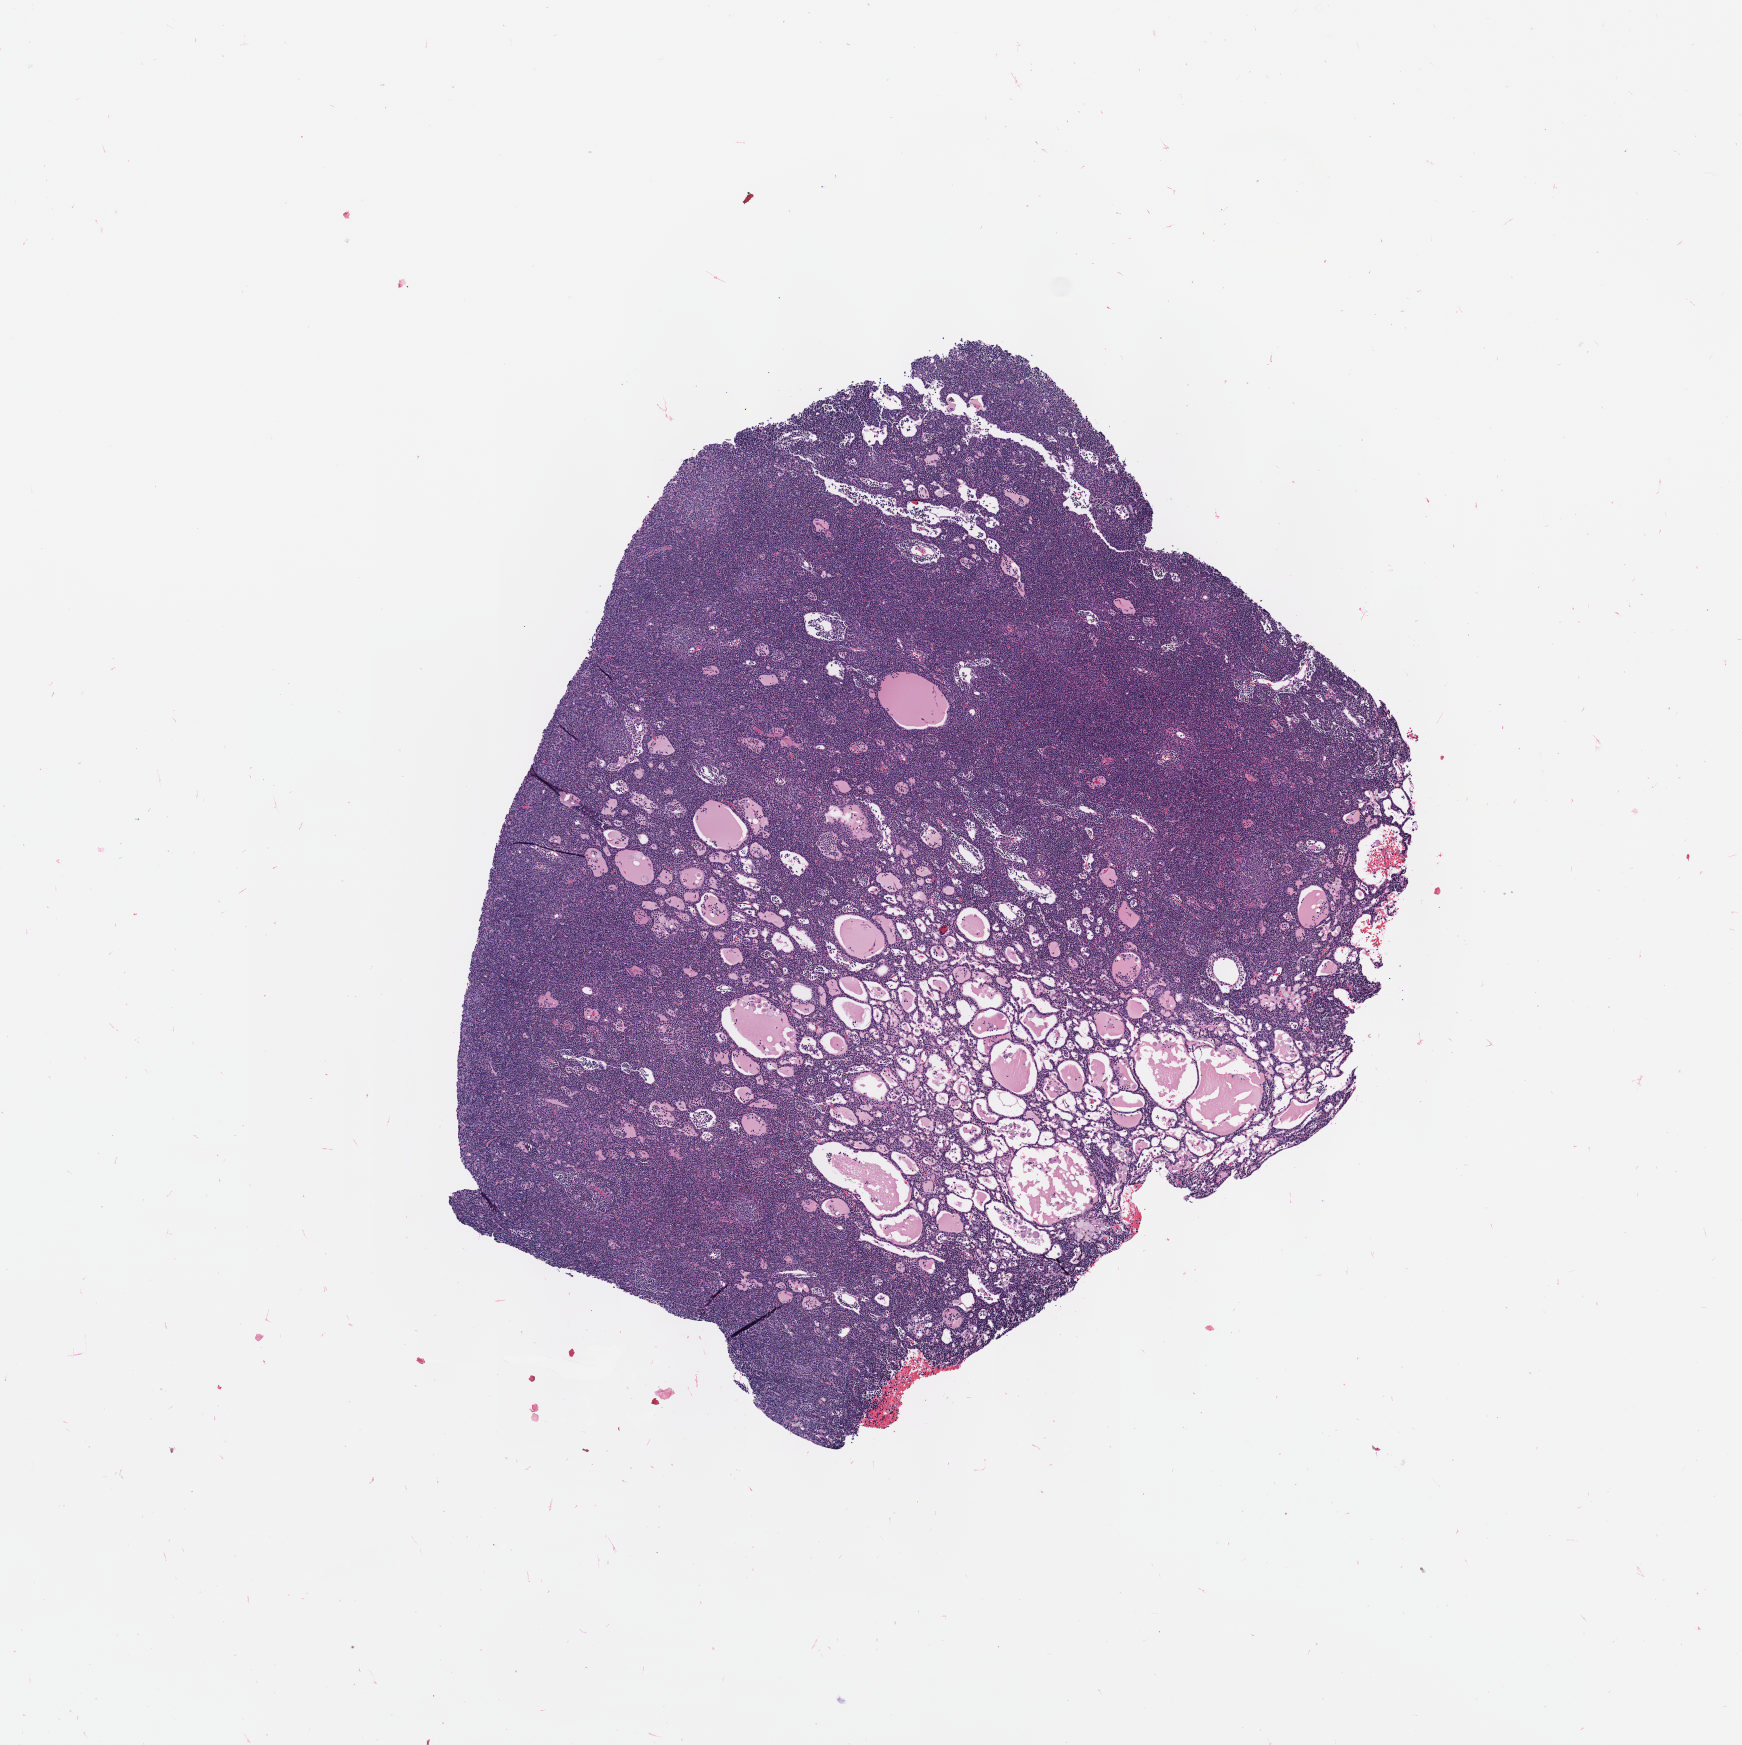
Digitized H&E tissue section (whole slide) — shown as a low-resolution overview of the whole scanned area (about 7.0 x 7.1 mm, slide scanned at 40x). Formalin-fixed paraffin-embedded (FFPE) diagnostic section. Sample: primary tumour, thymus. Female patient; age at initial diagnosis 35 years.
Diagnosis: Thymoma, type B2, malignant (anterior mediastinum).